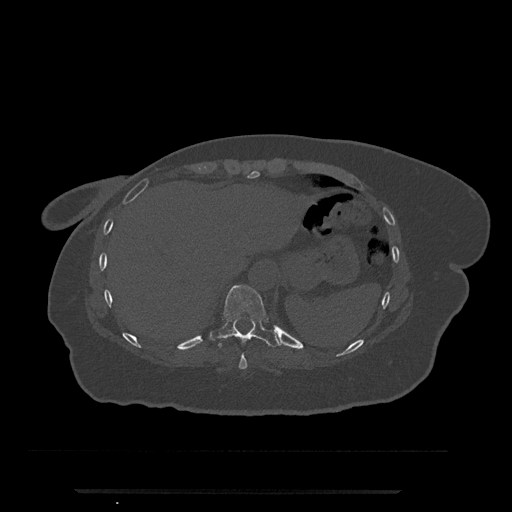
CT including the spine, one axial slice; position 298 of 797 along the scan axis; bone window (W 1800 / L 400 HU); 0.5 mm slice thickness; 512 × 512 image matrix, field of view 440 × 440 mm. Female patient, age 51 years. Case-level facts recorded for this patient, not image findings: primary cancer: neuro.
Structures marked on this image (semi-automatically segmented with operator editing):
- T10 vertebra: bounding box (x1, y1, x2, y2) in pixels: (211, 285, 279, 347)
- T9 vertebra: (238, 353, 247, 370)